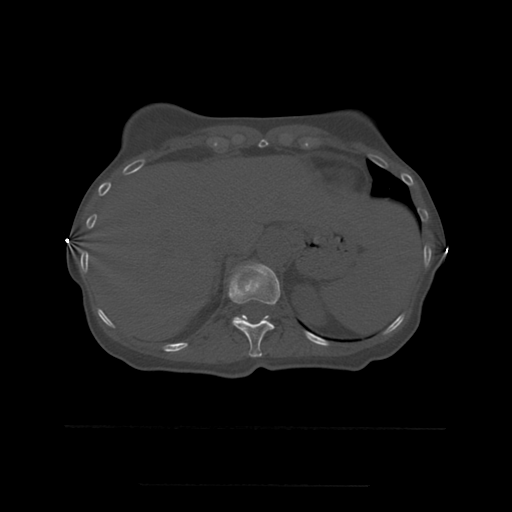
CT including the spine, one axial slice. Position 275 of 544 along the scan axis. Bone window (W 1800 / L 400 HU). 1.25 mm slice thickness. 512 × 512 image matrix, field of view 350 × 350 mm. Patient age 58 years. Case-level facts recorded for this patient, not image findings: primary cancer: lung.
Structures marked on this image (semi-automatic segmentation, software-assisted and operator-edited):
- T11 vertebra: bounding box <228,263,281,358> (left, top, right, bottom; pixels)
- T12 vertebra: <233,317,242,322>